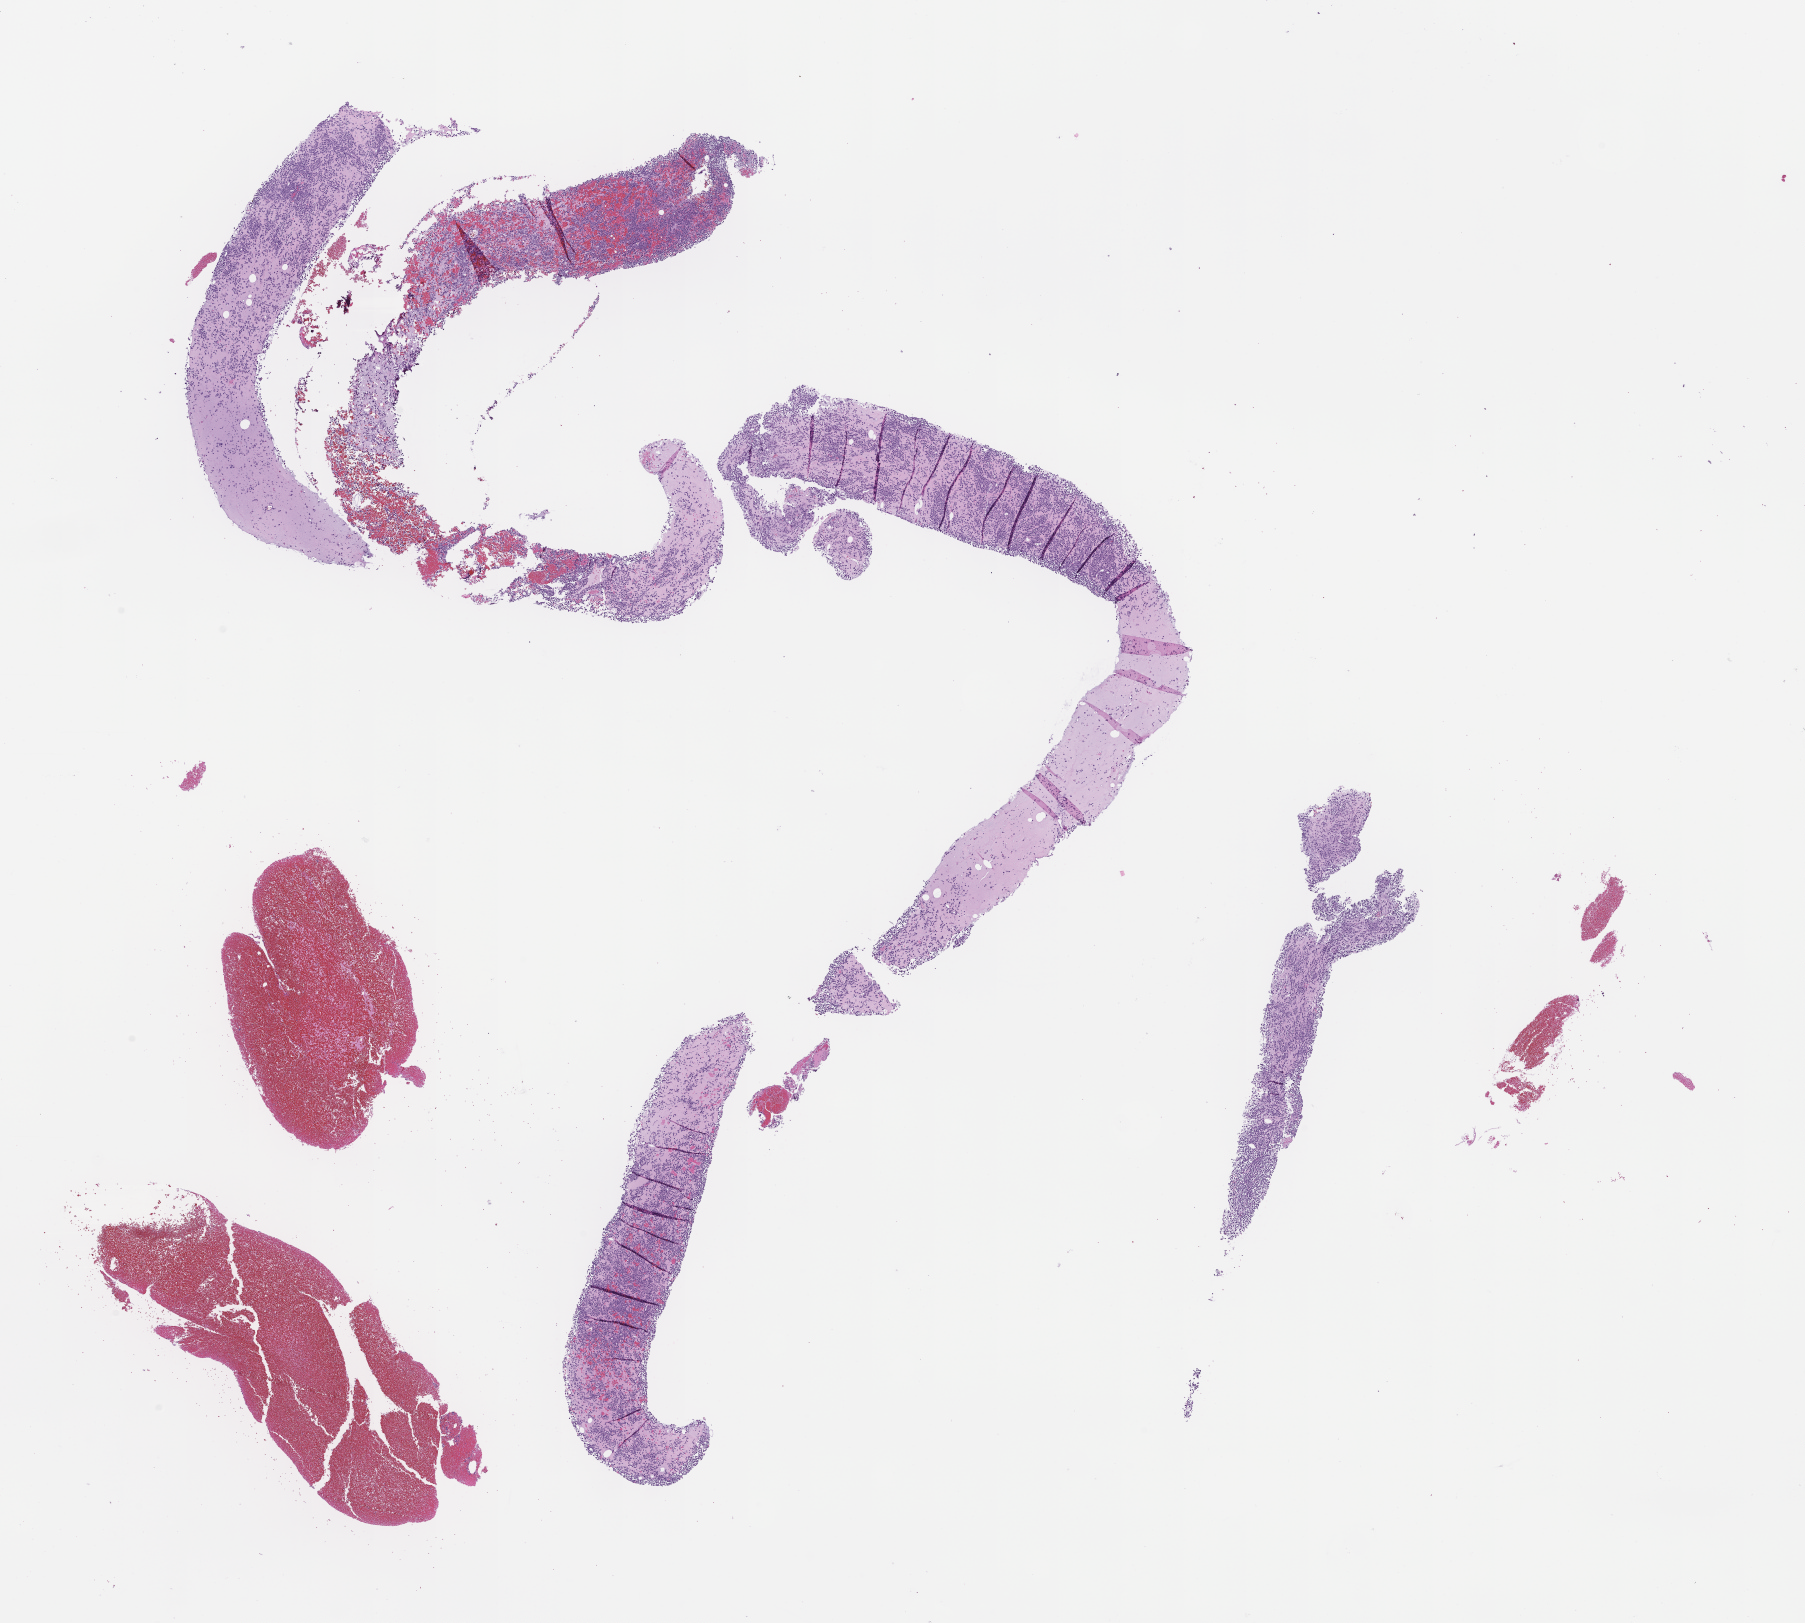
Haematoxylin and eosin whole-slide image — shown as a low-resolution overview of the whole scanned area (about 14.6 x 13.1 mm). Formalin-fixed paraffin-embedded section. Tissue site: bone marrow. Male patient.
This section: primary tumor. Diagnosis: Plasma Cell Myeloma.